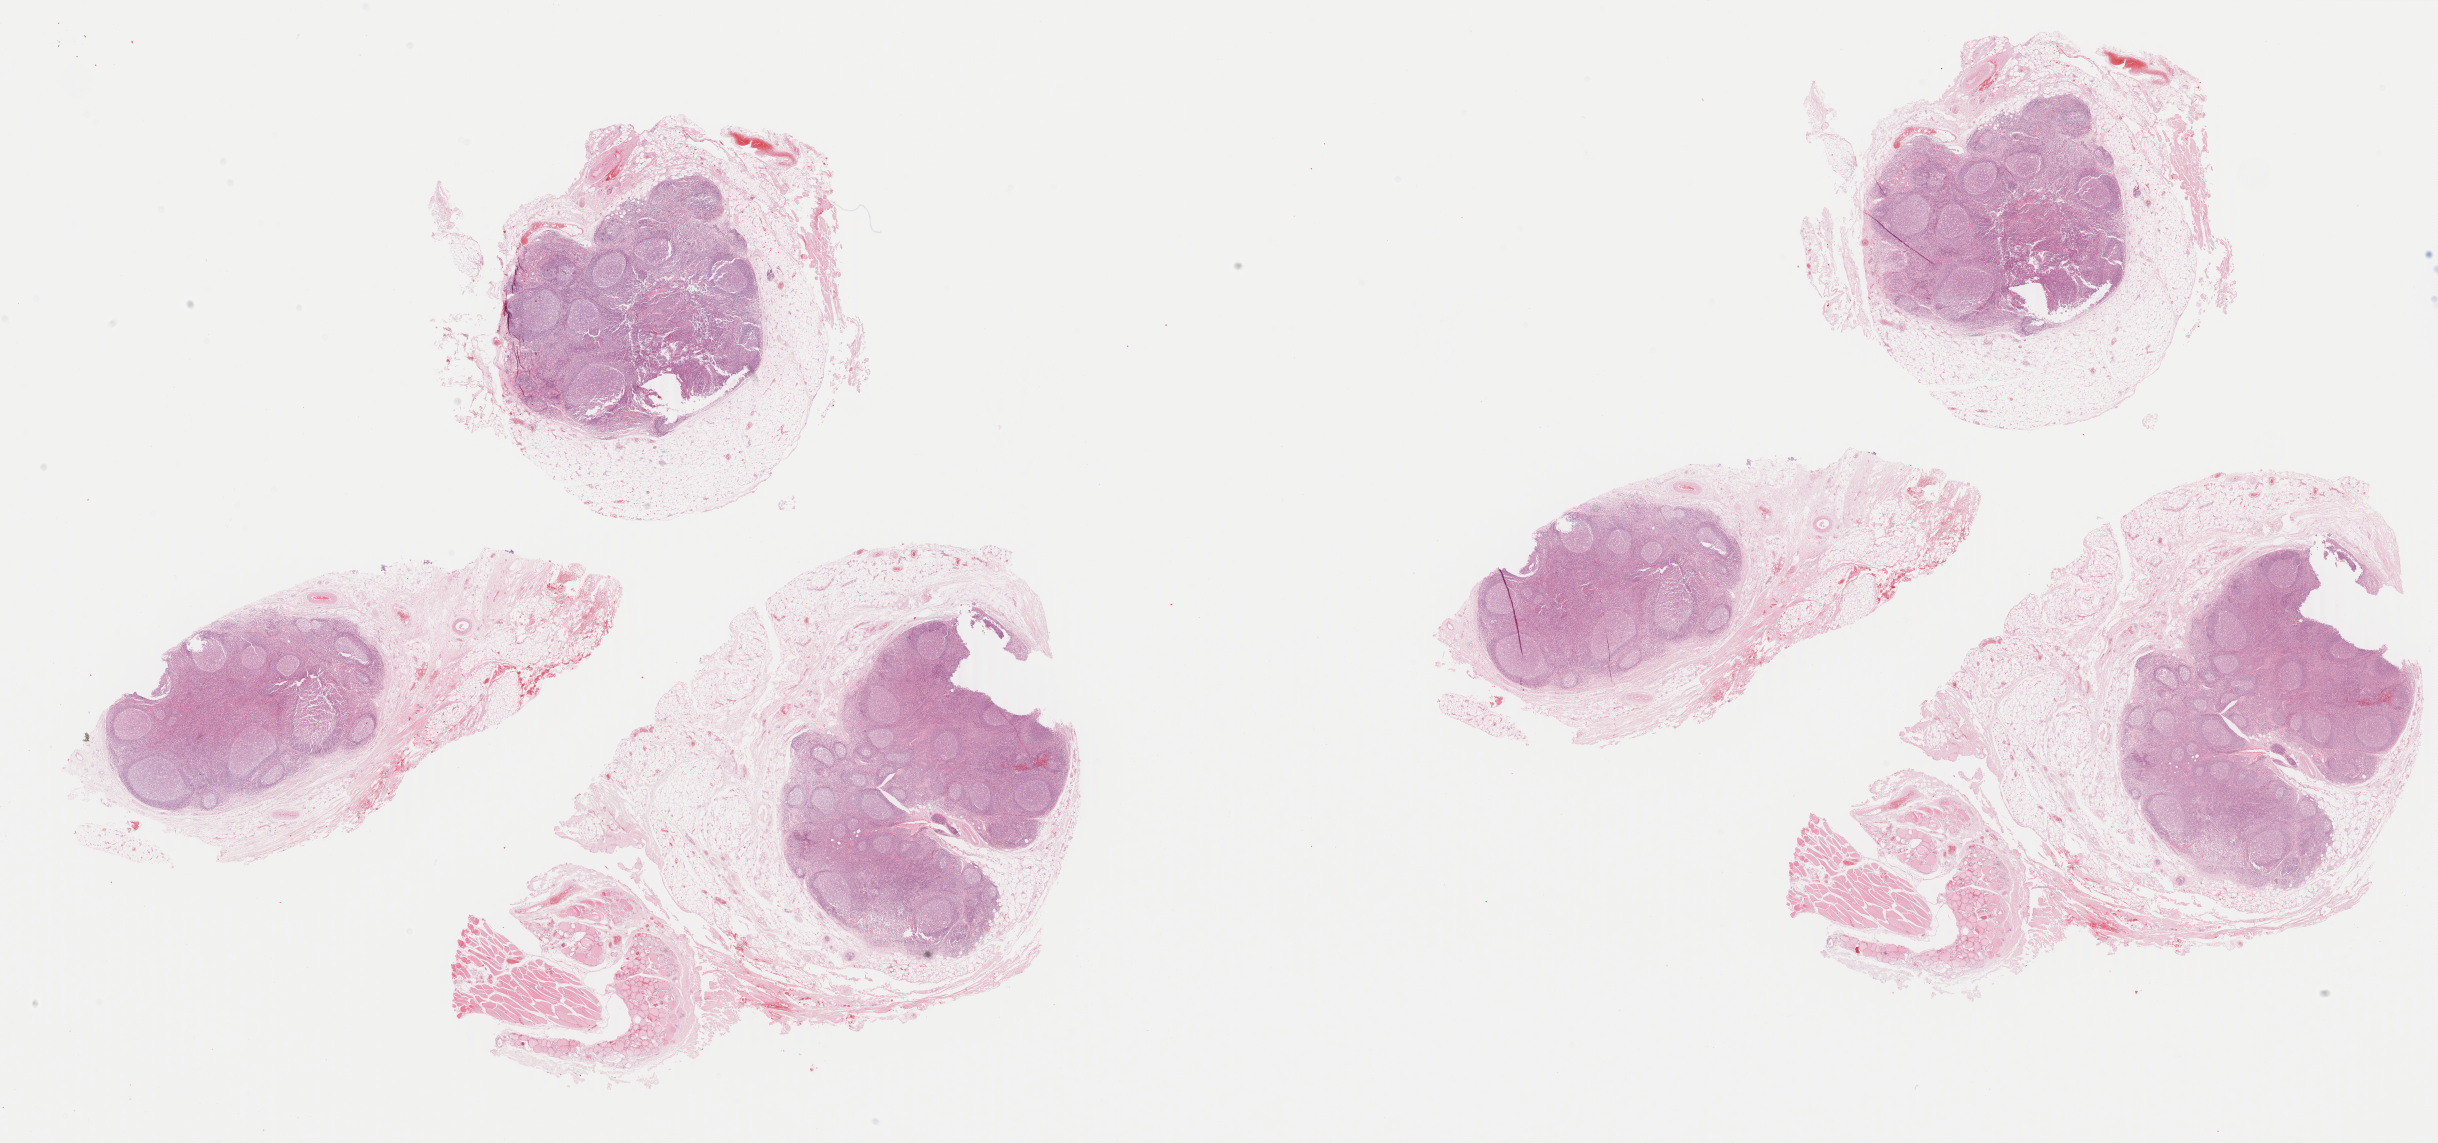
Digitized Hematoxylin and eosin (H&E) stained tissue section (whole slide) — whole scanned area (about 38.8 x 18.2 mm) shown as a low-resolution overview; formalin-fixed paraffin-embedded (FFPE) diagnostic section; primary tumour sample from the head and neck. Male patient; age at initial diagnosis 62 years. Histologic grade: G2 (moderately differentiated).
- diagnosis: Squamous cell carcinoma, keratinizing, NOS (larynx, NOS)
- lymph nodes positive (case pathology): 0 of 3 examined
- AJCC pathologic stage: II (7th edition)